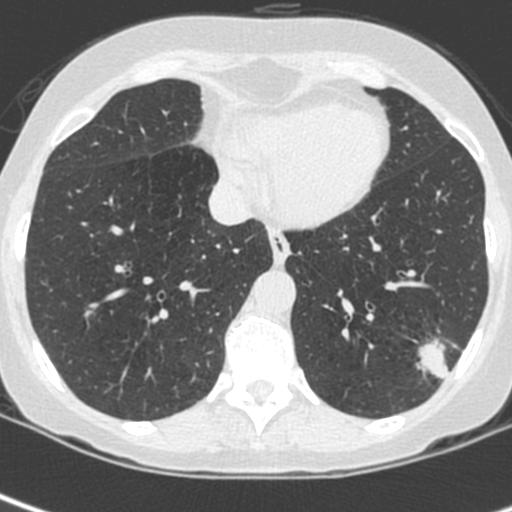
Chest CT (low-dose screening protocol), one axial image; first (baseline) screen; lung window (W 1500 / L -600 HU); 1.3 mm slice thickness; slice 162 of 252 in the series; 512 × 512 image matrix, field of view 271 × 271 mm. Female participant, aged 56 years at enrolment. Current smoker at enrolment.
• Lesion marked by an expert reader, box from (x=410, y=330) to (x=471, y=390) px.
• Reader record for this screening exam (exam-level; its link to the box is not recorded): non-calcified nodule or mass ≥4 mm, left lower lobe, 37 × 29 mm, spiculated (stellate) margins, ground glass attenuation.